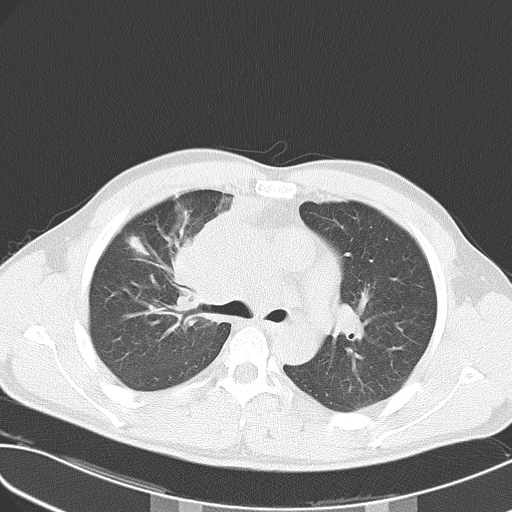
Chest CT, one axial slice. Slice 36 of 55 in the series (ordered by position). 120 kVp. Lung window (W 1500 / L -600 HU). 5 mm slice thickness. 512 × 512 image matrix. Male patient, age 32 years. From the clinical record (not read from this slice): clinical TNM (as recorded): T4 N3 M0.
Annotated regions visible in this slice (bounding box drawn by a radiologist):
- lung tumour (recorded histology: small cell carcinoma): box from (x=167, y=211) to (x=236, y=326) px